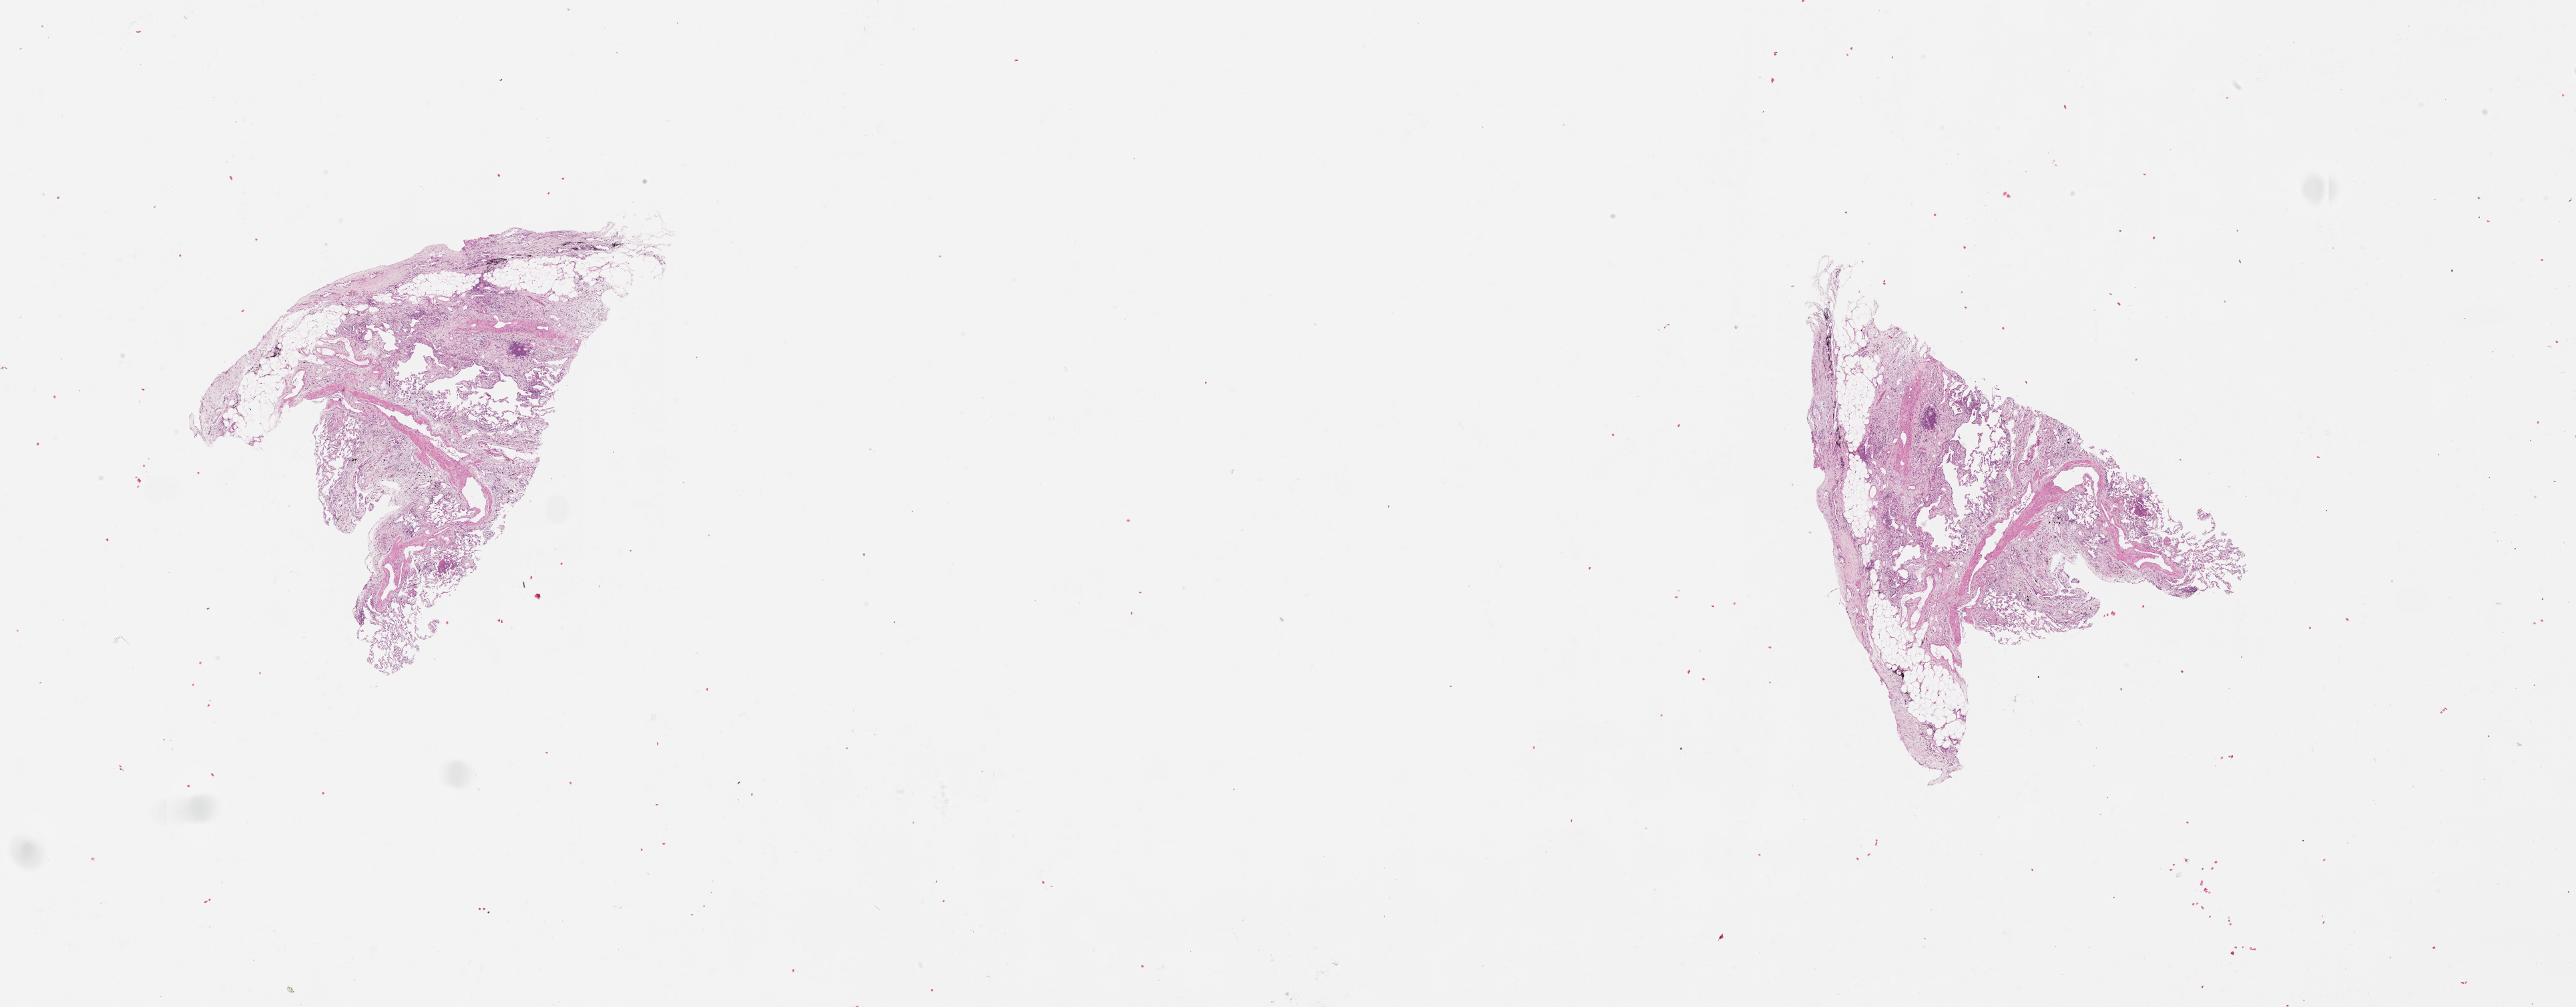
Whole-slide histology image, H&E, low-resolution overview of the scanned area, about 31.1 x 12.1 mm, normal (non-tumour) tissue sample, lung. 77-year-old male patient.
- this section: normal (non-tumour) tissue from the same patient
- patient diagnosis (cohort enrolment): squamous cell carcinoma (lung)